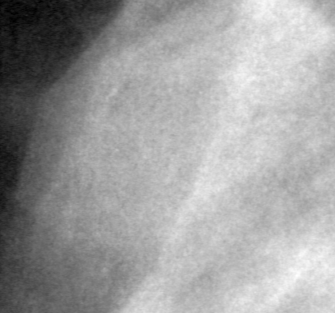
Cropped region of a digitized screen-film mammogram centred on a radiologist-marked abnormality; left breast; MLO view; BI-RADS breast density category 2 (scale 1–4).
Mass, shape oval, margins ill defined; BI-RADS assessment category 4; subtlety rating 4 on a 1 (subtle) to 5 (obvious) scale; pathology result (as recorded, not read from the image): malignant.